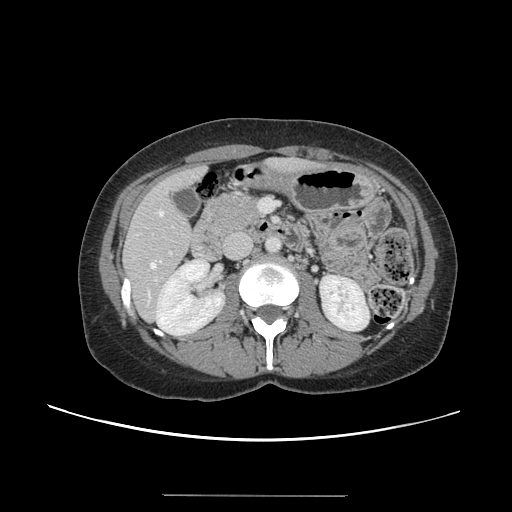
Contrast-enhanced abdominal CT, one axial slice; position 56 of 144 along the scan axis; 120 kVp; soft-tissue window (W 400 / L 40 HU); 512 × 512 image matrix. Female patient, age 53 years. Case-level facts recorded for this patient, not image findings: diagnosis: colorectal cancer liver metastases, imaged before liver resection; multiple liver metastases: yes; largest metastasis: 1.1 cm; disease in both lobes: no.
Annotated regions visible in this slice (expert manual segmentation):
- hepatic veins: bounding box <151,212,163,268> (left, top, right, bottom; pixels)
- liver: <124,159,315,318>
- planned liver remnant (the part of the liver to remain after resection): <125,159,314,312>
- portal vein (with intrahepatic branches): <154,251,172,282>